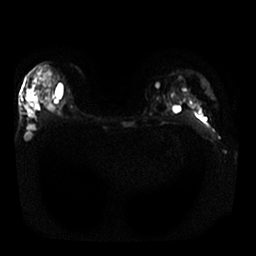
Breast MRI, one axial slice. Diffusion-weighted series; image 2 of 4 stored at this slice position (different b-values; order by instance number). 1.5 T. 4 mm slice thickness. 256 × 256 image matrix, field of view 340 × 340 mm. Female patient.
Structures marked on this image (outlined manually by an expert reader):
- tumour on diffusion-weighted imaging: box from (x=40, y=69) to (x=50, y=82) px